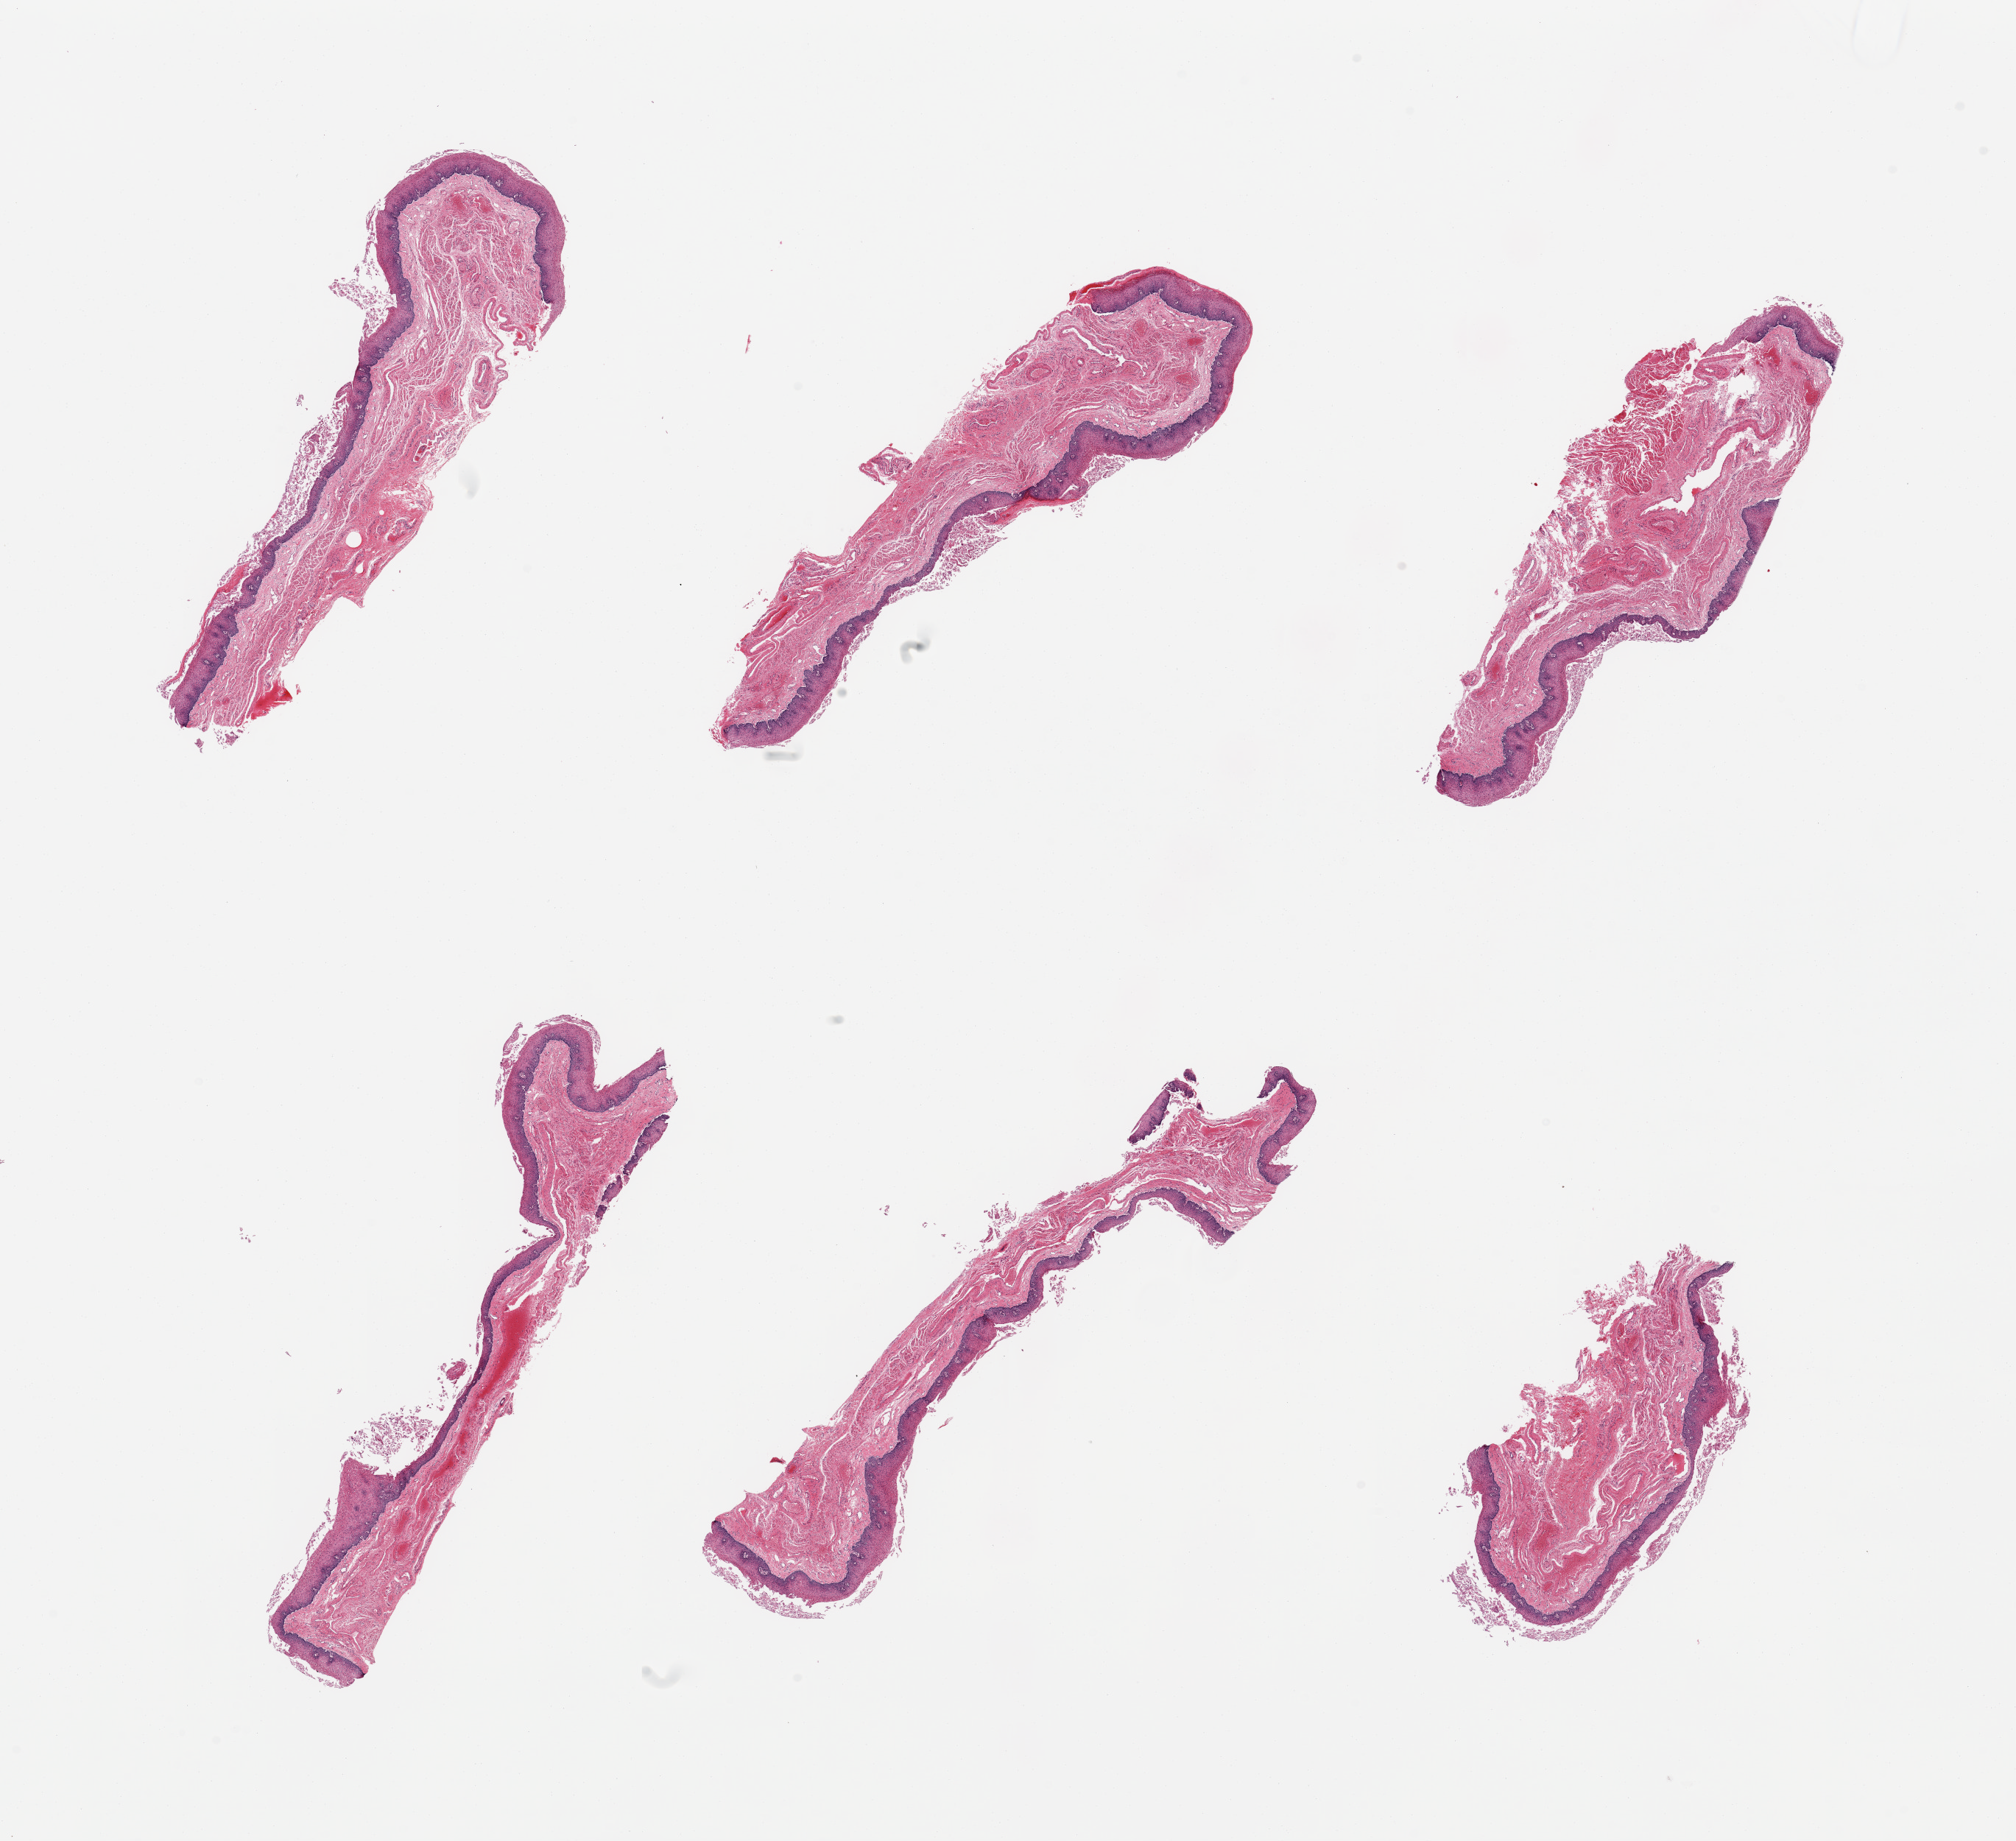
Whole-slide image, H&E stain — low-resolution overview of the scanned area, about 21.7 x 19.8 mm; PAXgene-fixed, paraffin-embedded tissue; section of esophageal mucous membrane (target tissue); donor tissue sample. Donor sex: female.
Review note (as recorded): 6 pieces; epithelium is partially sloughing, small focus of muscularis (not target); ectatic, thick-walled vessels c/w varices.